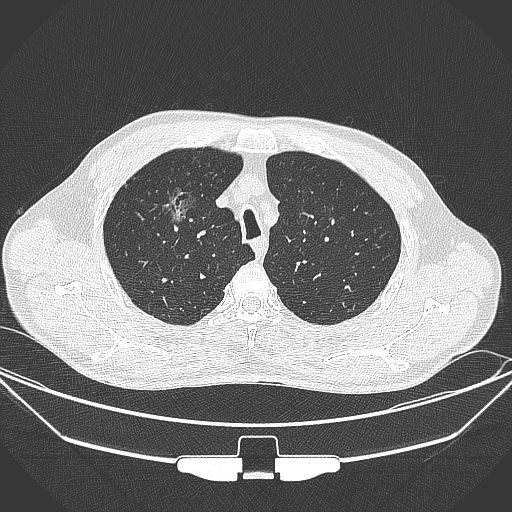
Chest CT, one axial slice. Slice 277 of 355 in the series (ordered by position). 120 kVp. Lung window (W 1500 / L -600 HU). 1 mm slice thickness. 512 × 512 image matrix, field of view 399 × 399 mm. Patient: male, 67 years. Case-level facts recorded for this patient, not image findings: clinical TNM (as recorded): T1c N0 M0; histopathological grade: G2.
Structures marked on this image (bounding box drawn by a radiologist):
- lung tumour (recorded histology: adenocarcinoma): box from (x=159, y=185) to (x=208, y=236) px